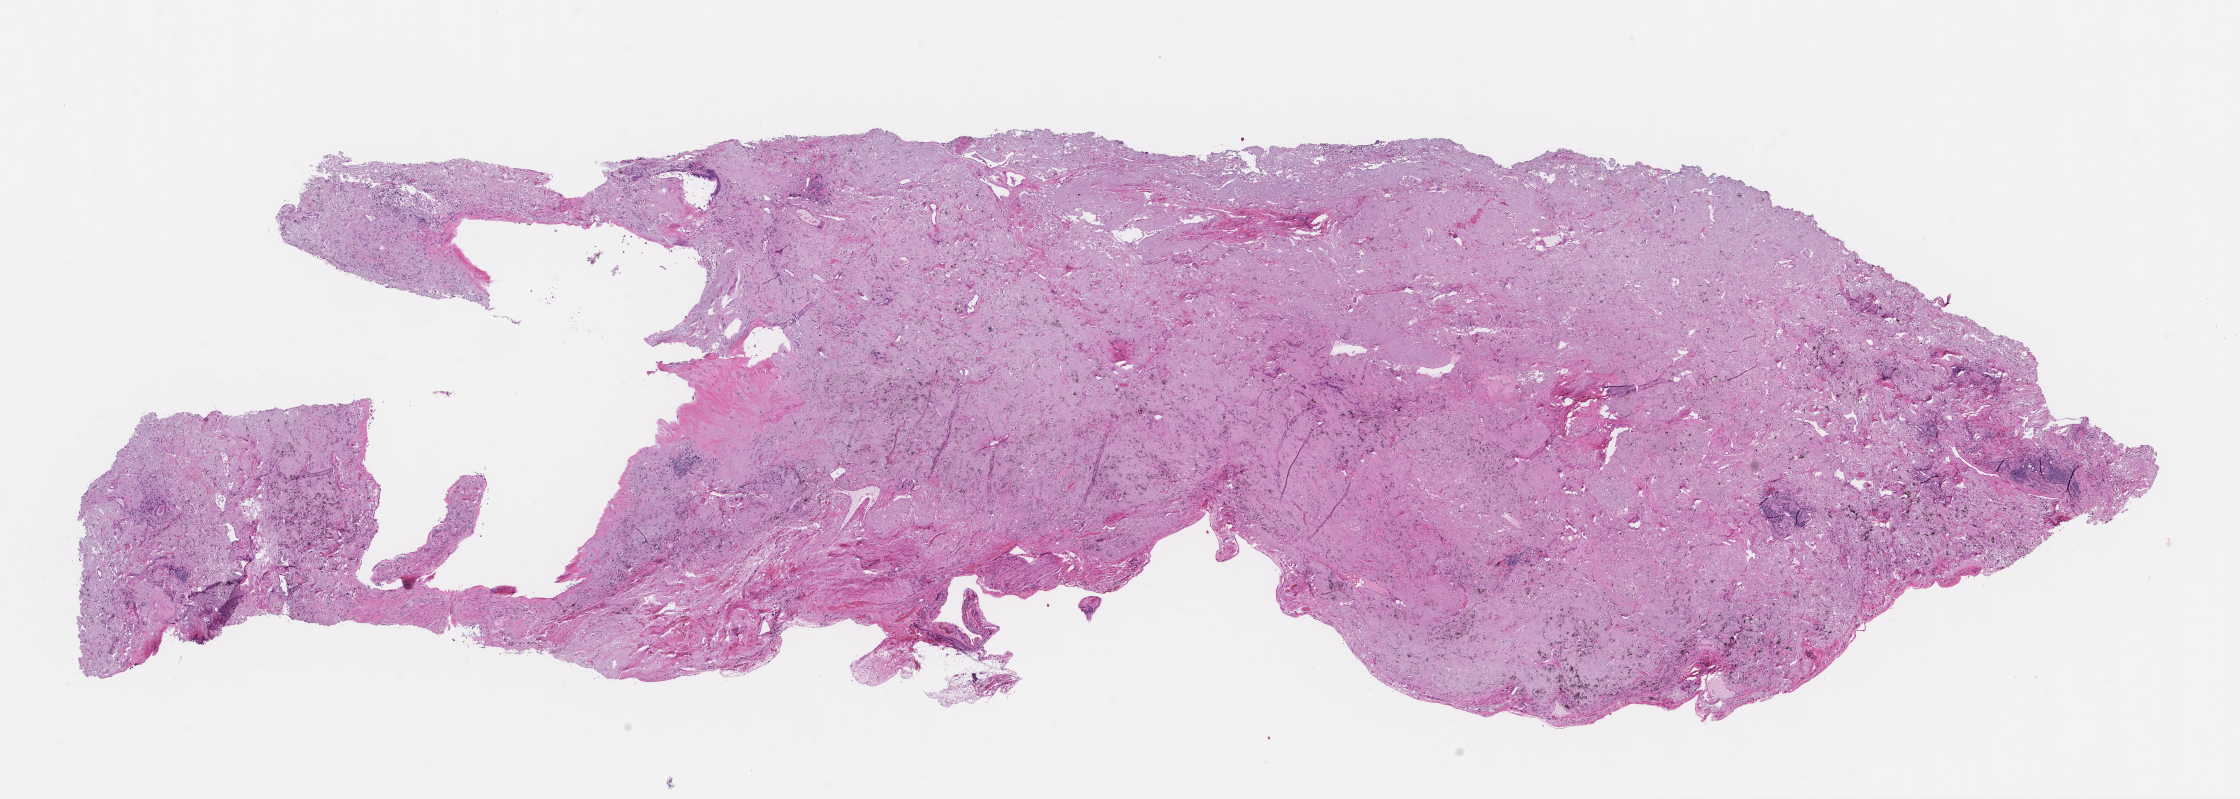
Whole-slide image, hematoxylin and eosin (H&E) stain — low-resolution overview of the scanned area, about 18.1 x 6.5 mm, formalin-fixed paraffin-embedded section, tissue site: lung, specimen time point: collected at baseline (before treatment). Male patient.
This section: primary tumor. Diagnosis: Non-Small Cell Lung Carcinoma.